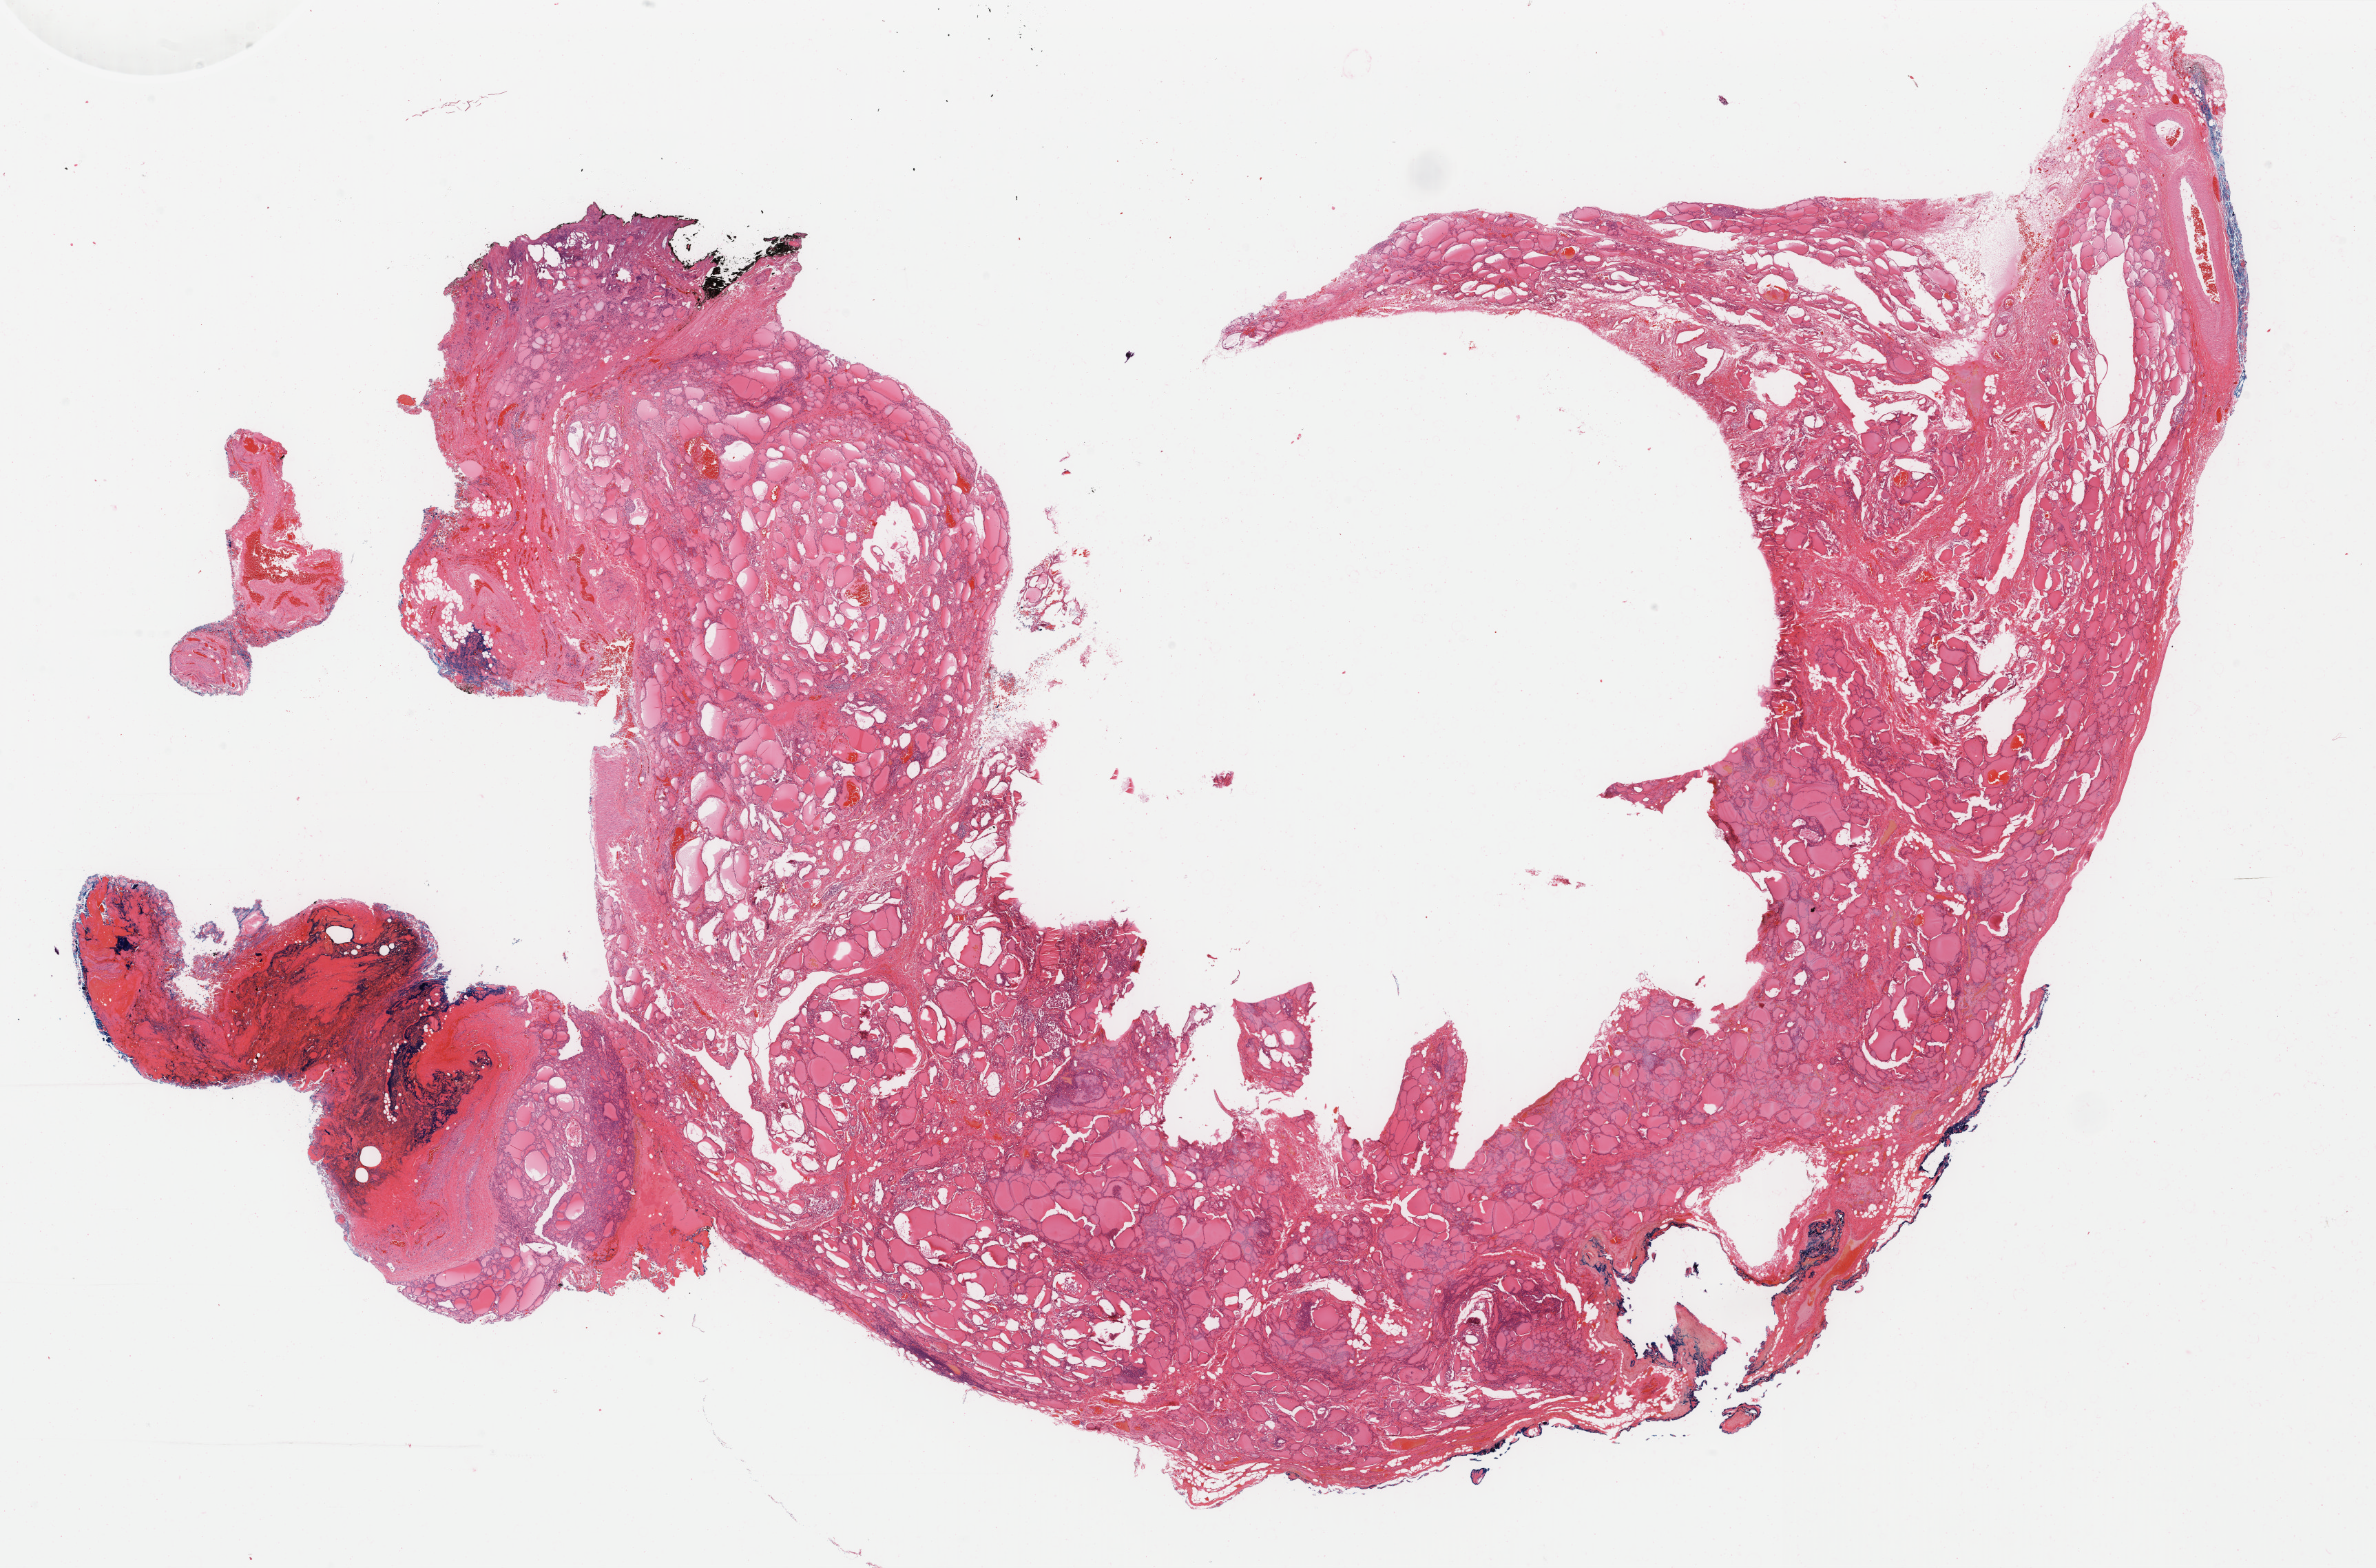
H&E whole-slide image, a low-resolution overview of the entire scanned area, about 27.4 x 18.1 mm (acquisition: 40x scan); FFPE section; primary tumour sample from the thyroid. Female patient; age at initial diagnosis 55 years.
TNM: T3 N0 M0. Lymph nodes positive (case pathology): 0 of 1 examined. Pathologic diagnosis: Papillary carcinoma, follicular variant (thyroid gland). AJCC pathologic stage: III (7th edition). Laterality: right.